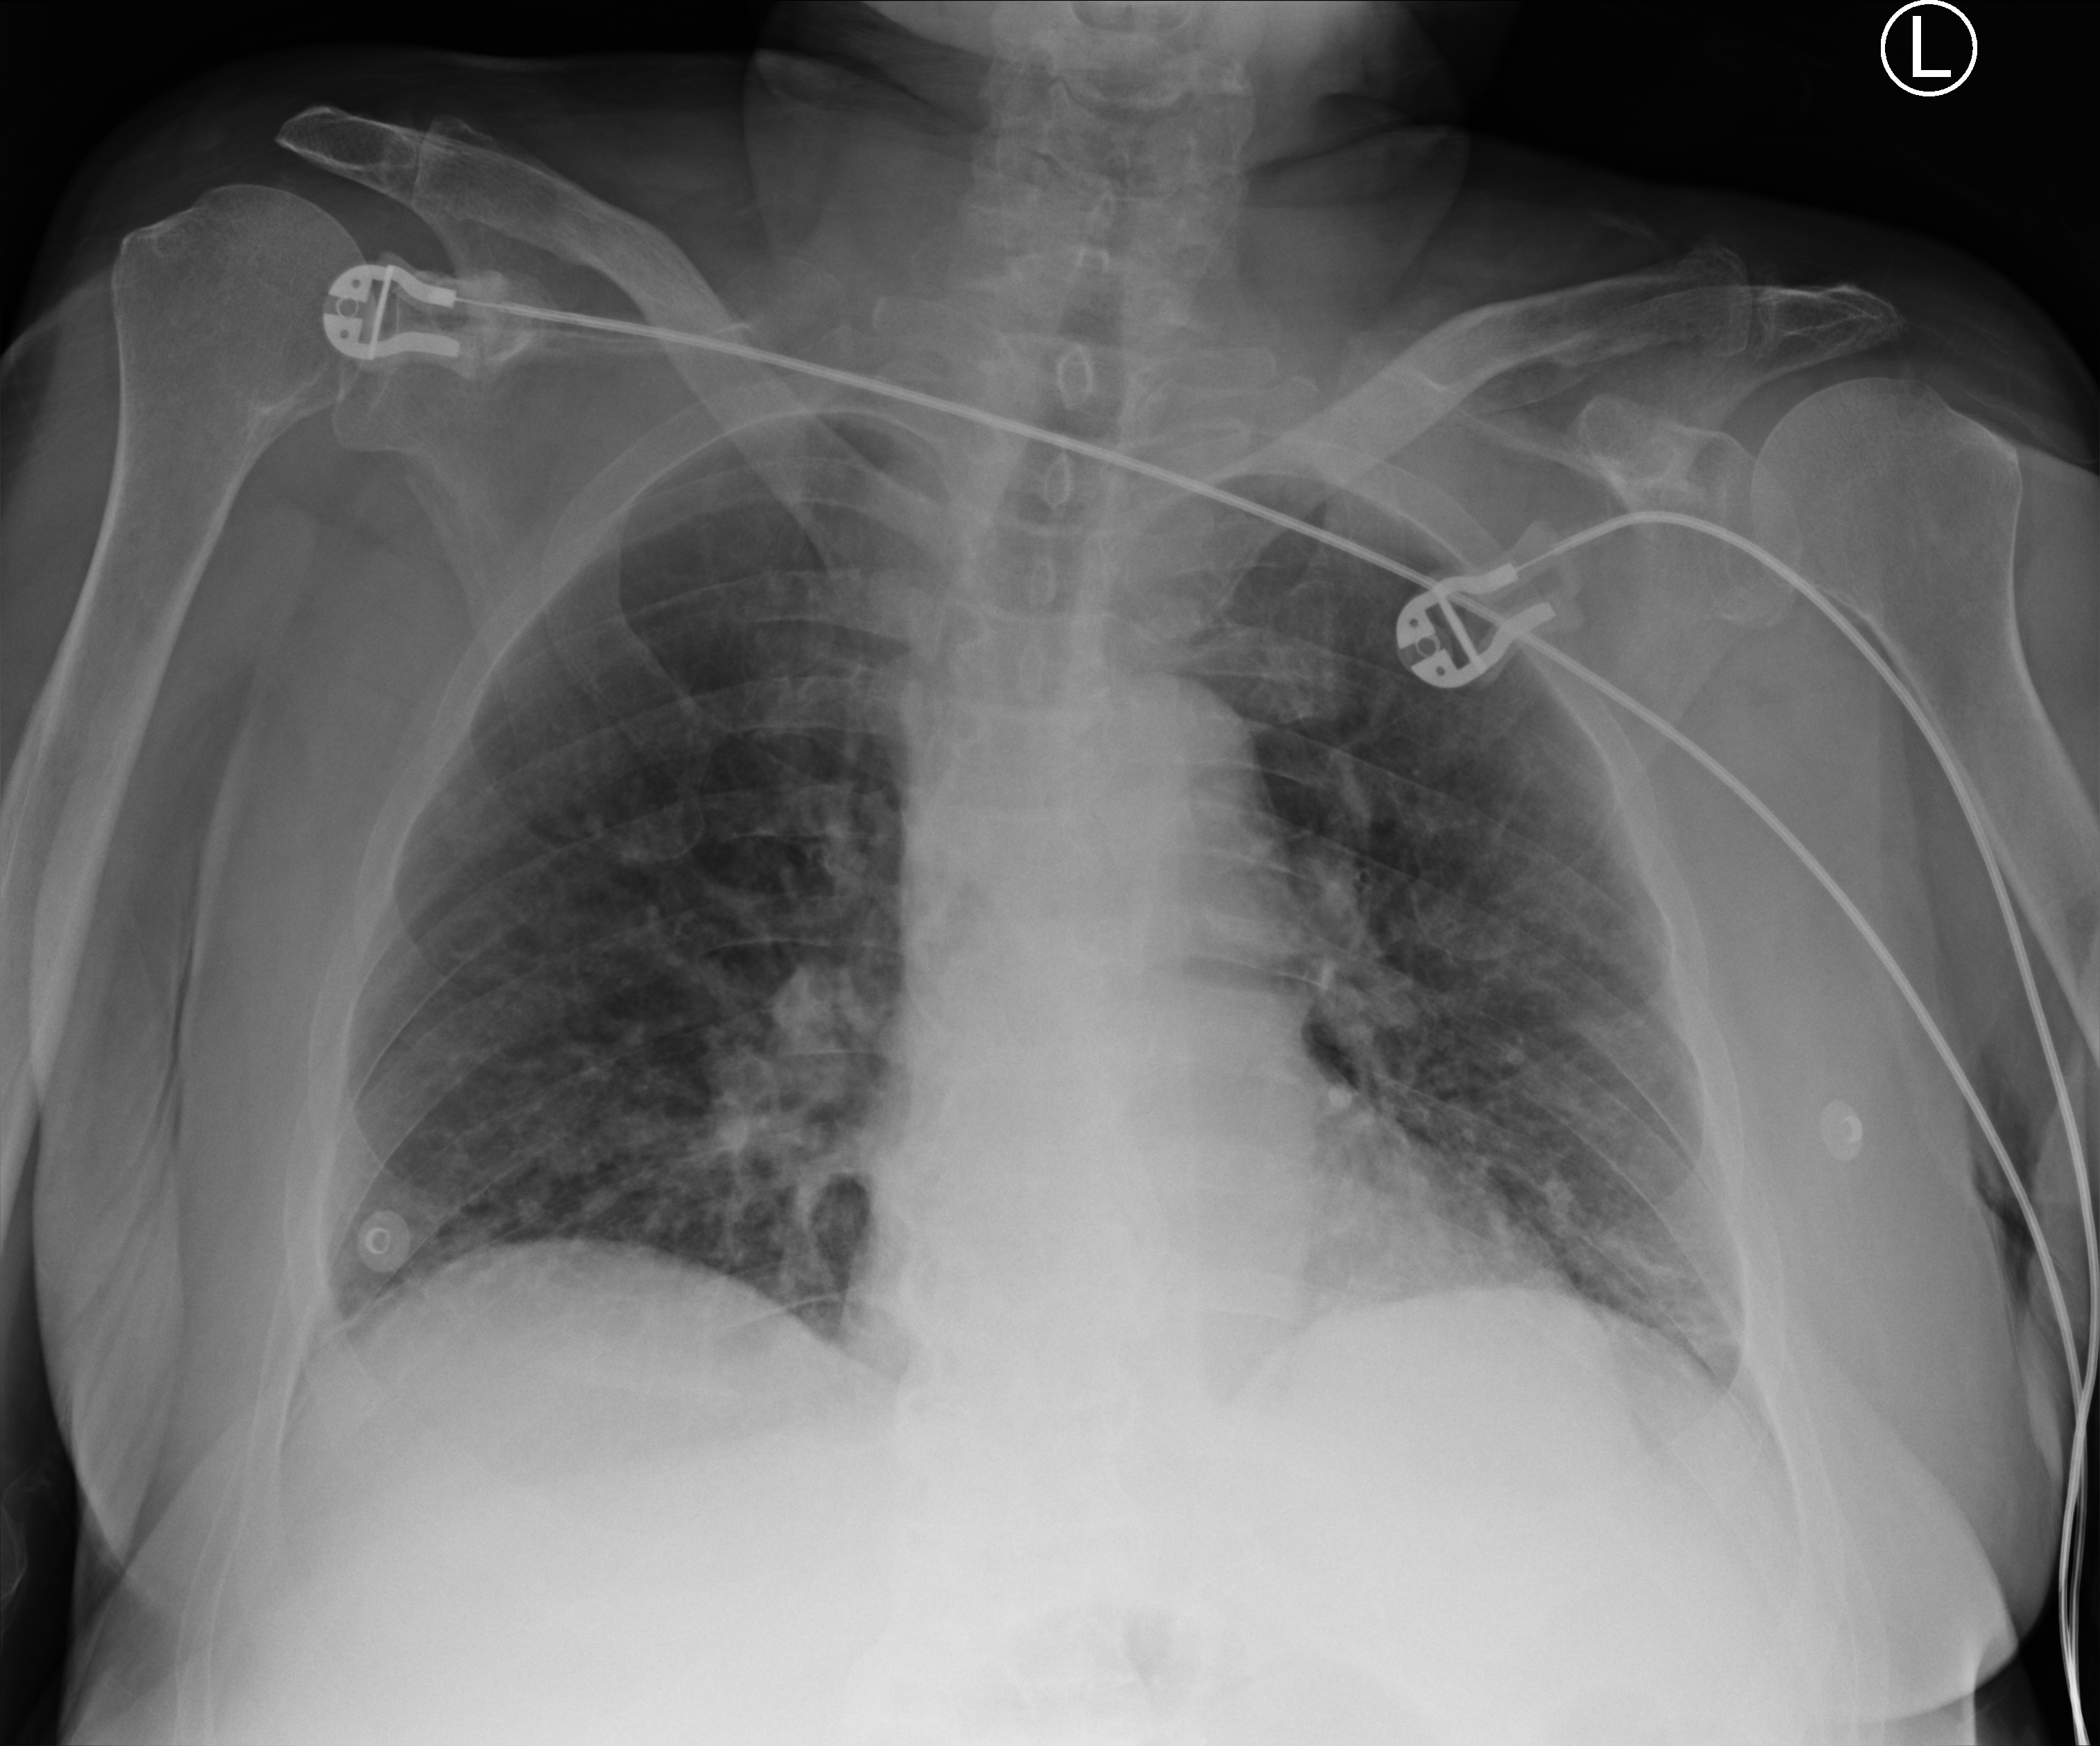
Chest X-ray (portable); anteroposterior (AP) projection. Patient hospitalised with COVID-19; male, aged 60–74 years.
From the hospital-stay record, not from the radiograph (when in the stay this image was taken is not recorded): admitted to intensive care during this hospital stay: no.